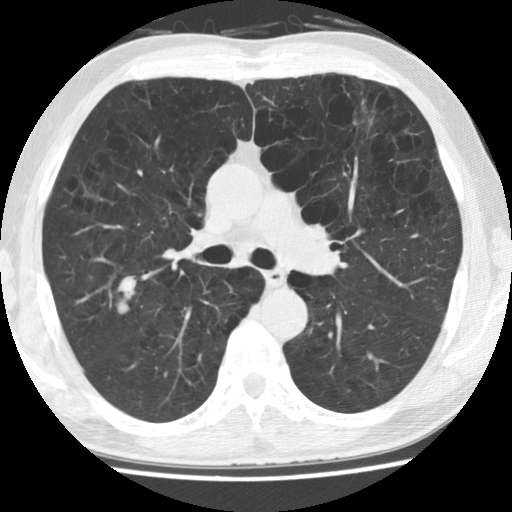
Low-dose screening chest CT, axial slice. Baseline annual screen. Lung window (W 1500 / L -600 HU). Slice 65 of 158 in the series. Male, age 62 years at enrolment. Current smoker at enrolment.
Lesion marked by an expert reader, box from (x=94, y=262) to (x=150, y=324) px. The screening reader recorded 2 non-calcified nodules or masses ≥4 mm on this exam (left upper lobe, right upper lobe); which of them this box marks is not recorded. Official screen result: positive, change unspecified: nodule(s) >= 4 mm or enlarging nodule(s), mass(es), or other non-specific abnormalities suspicious for lung cancer. Later outcome: lung cancer diagnosed 288 days after this screen — oat cell carcinoma, right upper lobe, undifferentiated (G4), stage IV (AJCC 6th edition), 30 mm at pathology.